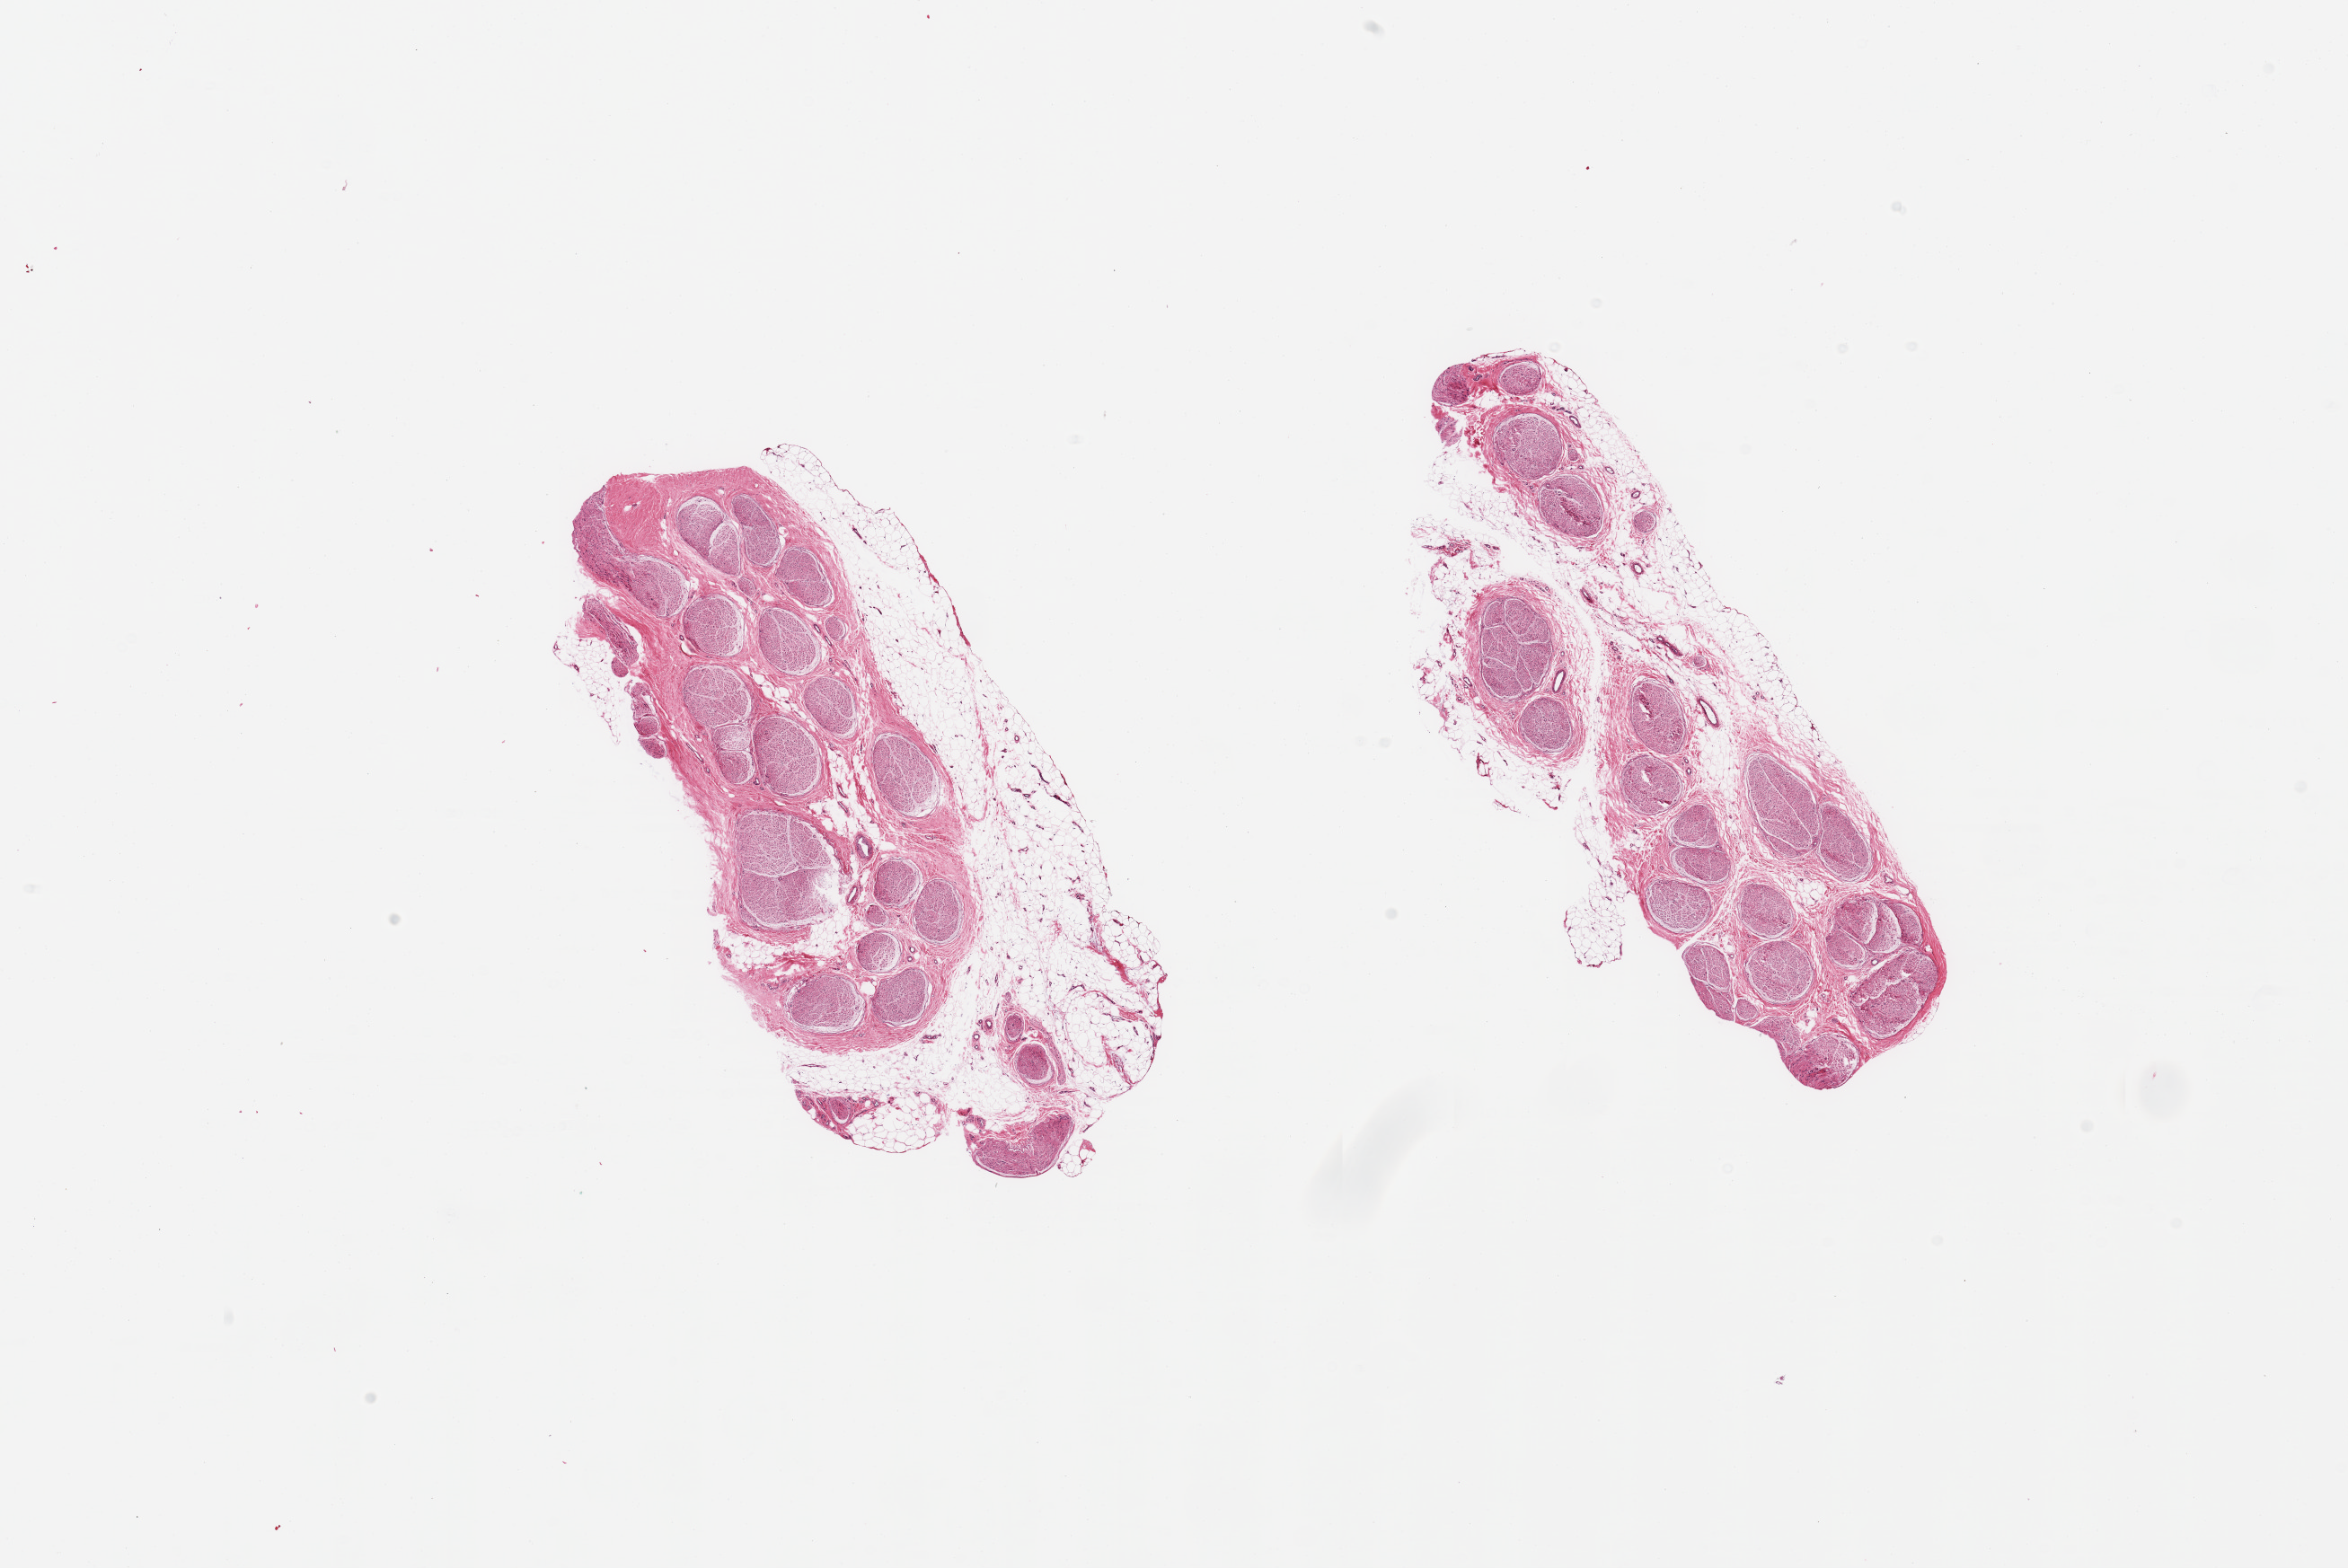
Whole-slide image, hematoxylin and eosin (H&E) stain — shown as a low-resolution overview of the whole scanned area (about 20.7 x 13.8 mm); PAXgene-fixed, paraffin-embedded tissue; sampled site (target tissue): tibial nerve; tissue donor sample. Donor sex: male.
• reviewer comment on this tissue sample: 2 pieces; partial rim of adherent fat up to ~0.7mm